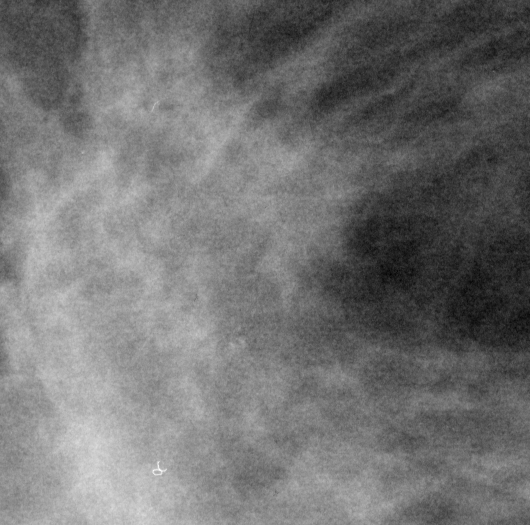
Crop from a digitized film mammogram around one marked abnormality; left breast; MLO view; BI-RADS breast density category 2 (scale 1–4).
- Mass, shape irregular, margins spiculated; BI-RADS assessment category 5; subtlety rating 4 on a 1 (subtle) to 5 (obvious) scale; pathology result (as recorded, not read from the image): malignant.